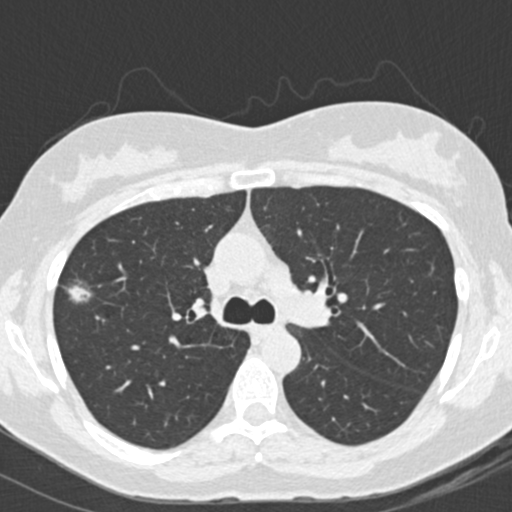
Low-dose screening chest CT, one axial slice; reconstruction kernel B30f; lung window (W 1500 / L -600 HU); 512 × 512 image matrix, field of view 290 × 290 mm.
Outlined on this slice (expert manual segmentation):
- lesion 1 (tumor, upper lobe of right lung): bounding box <68,282,92,303> (left, top, right, bottom; pixels)